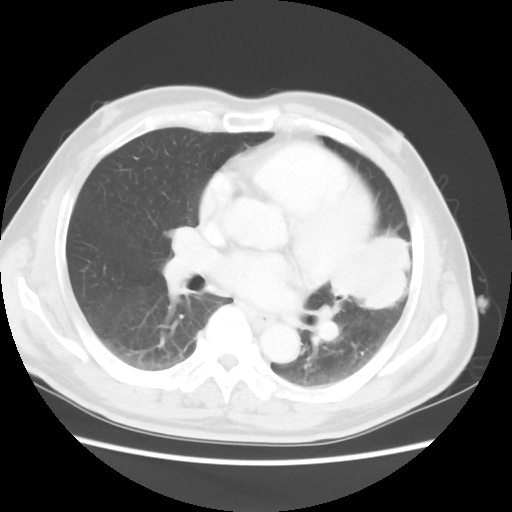
Chest CT, one axial slice. Slice 25 of 50 in the series (ordered by position). 120 kVp. Lung window (W 1500 / L -600 HU). 5 mm slice thickness. 512 × 512 image matrix, field of view 360 × 360 mm. Patient: male, 69 years. From the clinical record (not read from this slice): clinical TNM (as recorded): T3 N1 M1a.
Outlined on this slice (bounding box drawn by a radiologist):
- lung tumour (recorded histology: squamous cell carcinoma): bounding box [x1, y1, x2, y2] px = [329, 218, 434, 325]